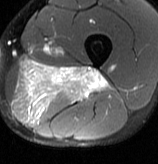
MRI of an extremity soft-tissue mass, one axial slice; position 32 of 70 along the scan axis; T2-weighted fat-saturated; MR volume resampled by the dataset authors to the PET/CT grid (not the native acquisition matrix); 3.27 mm slice thickness; 158 × 164 image matrix. Male patient. From the clinical record (not read from this slice): histological type: extraskeletal osteosarcoma; grade: high; site of the primary tumour: left adductur.
Outlined on this slice (expert contour drawn on MRI and transferred to this co-registered scan by the dataset authors):
- gross tumour volume (mass): box from (x=11, y=59) to (x=110, y=125) px